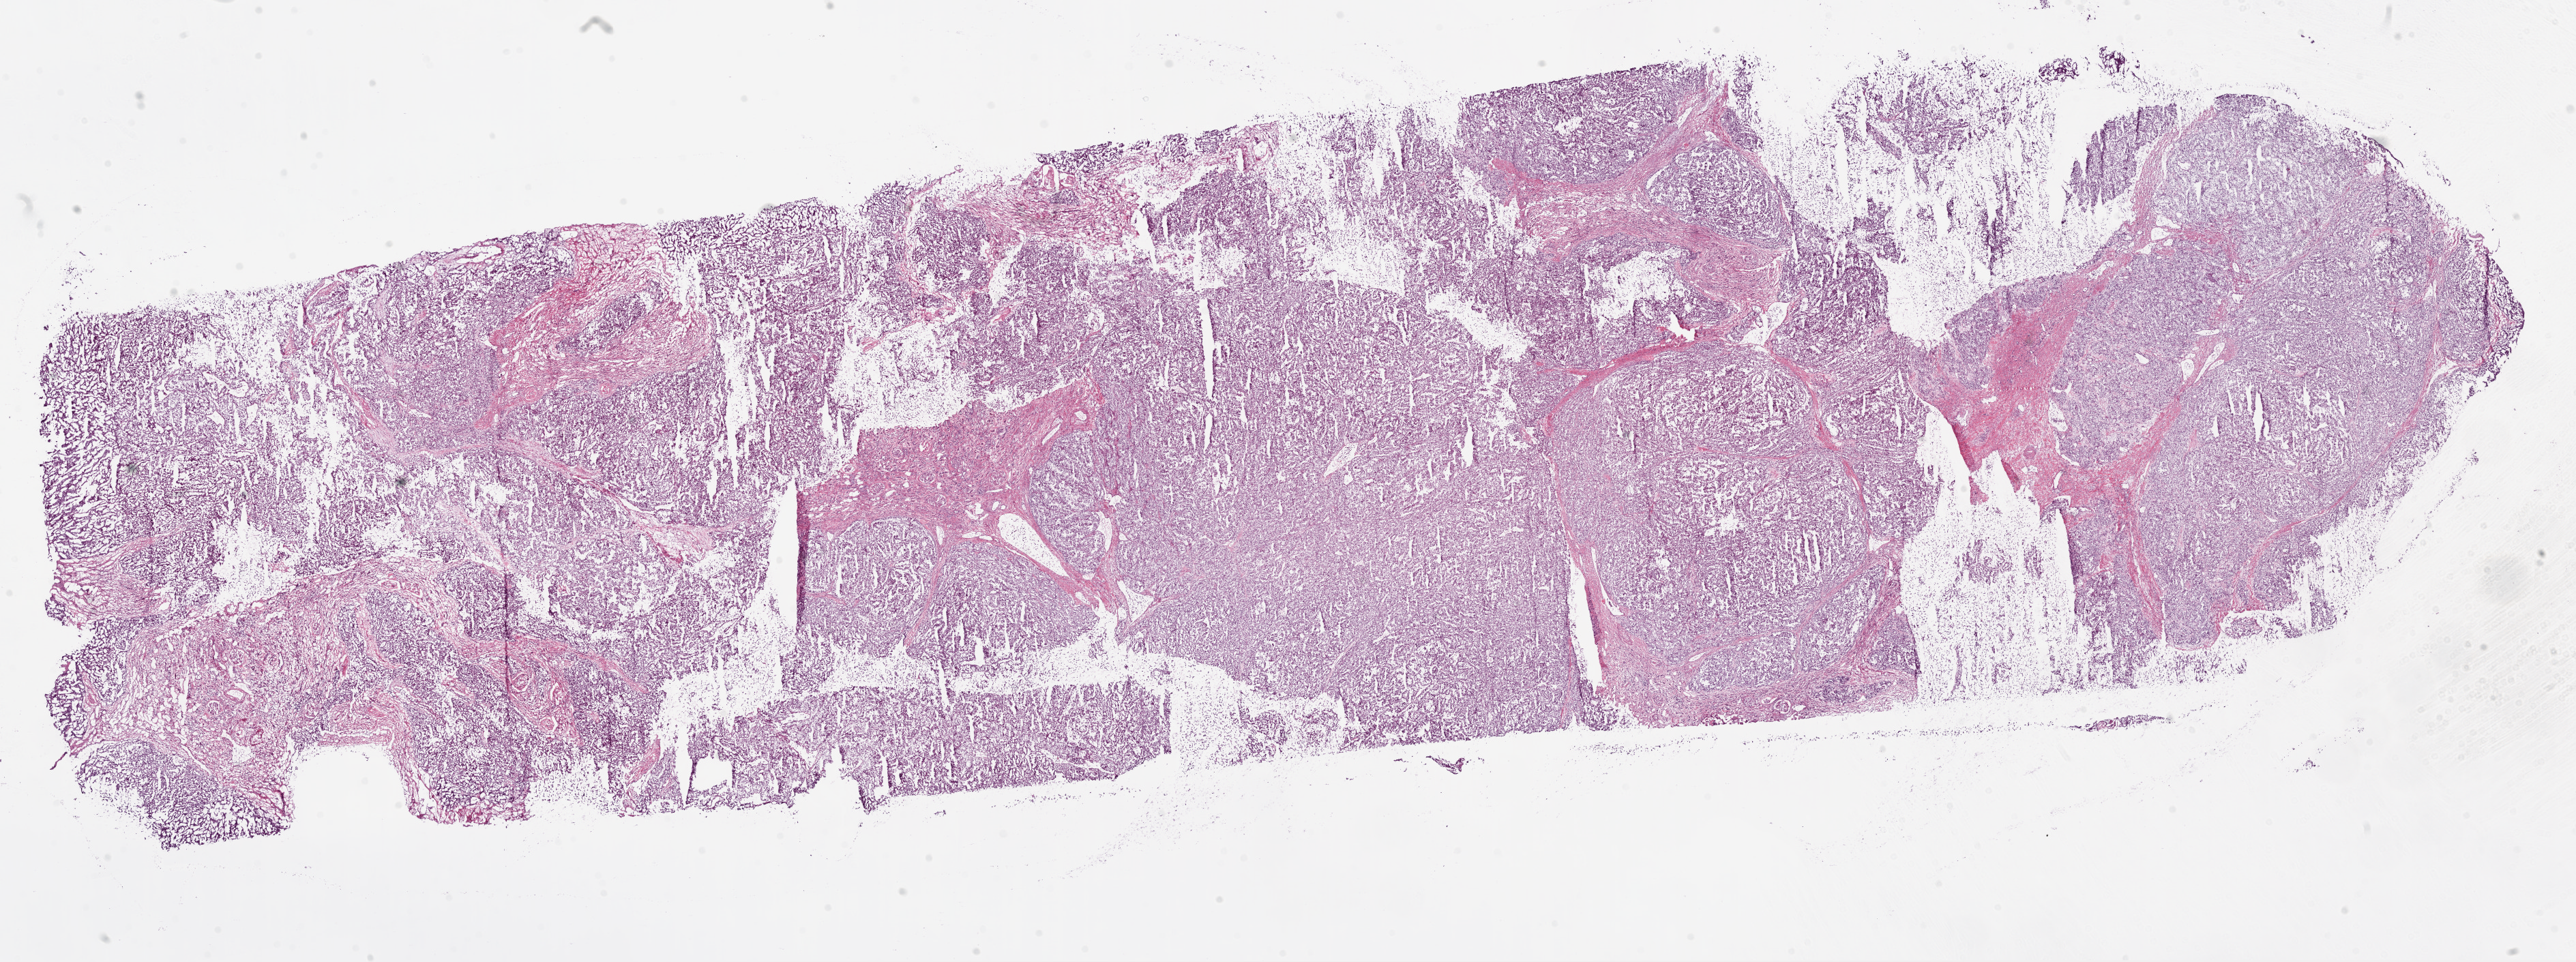
Whole-slide histology image, Hematoxylin and eosin (H&E) stained, a low-resolution overview of the entire scanned area, about 30.5 x 11.4 mm. Frozen section from the bottom of the tissue portion. Sample: primary tumour, kidney. Female patient; age at initial diagnosis 65 years. Histologic grade: G4 (undifferentiated). Pathologist review of this section (percent, as recorded): tumour cells 85%, tumour nuclei 85%, normal cells 0%, stromal cells 15%, necrosis 0%.
* AJCC pathologic stage: IV
* laterality: right
* diagnosis: Clear cell adenocarcinoma, NOS